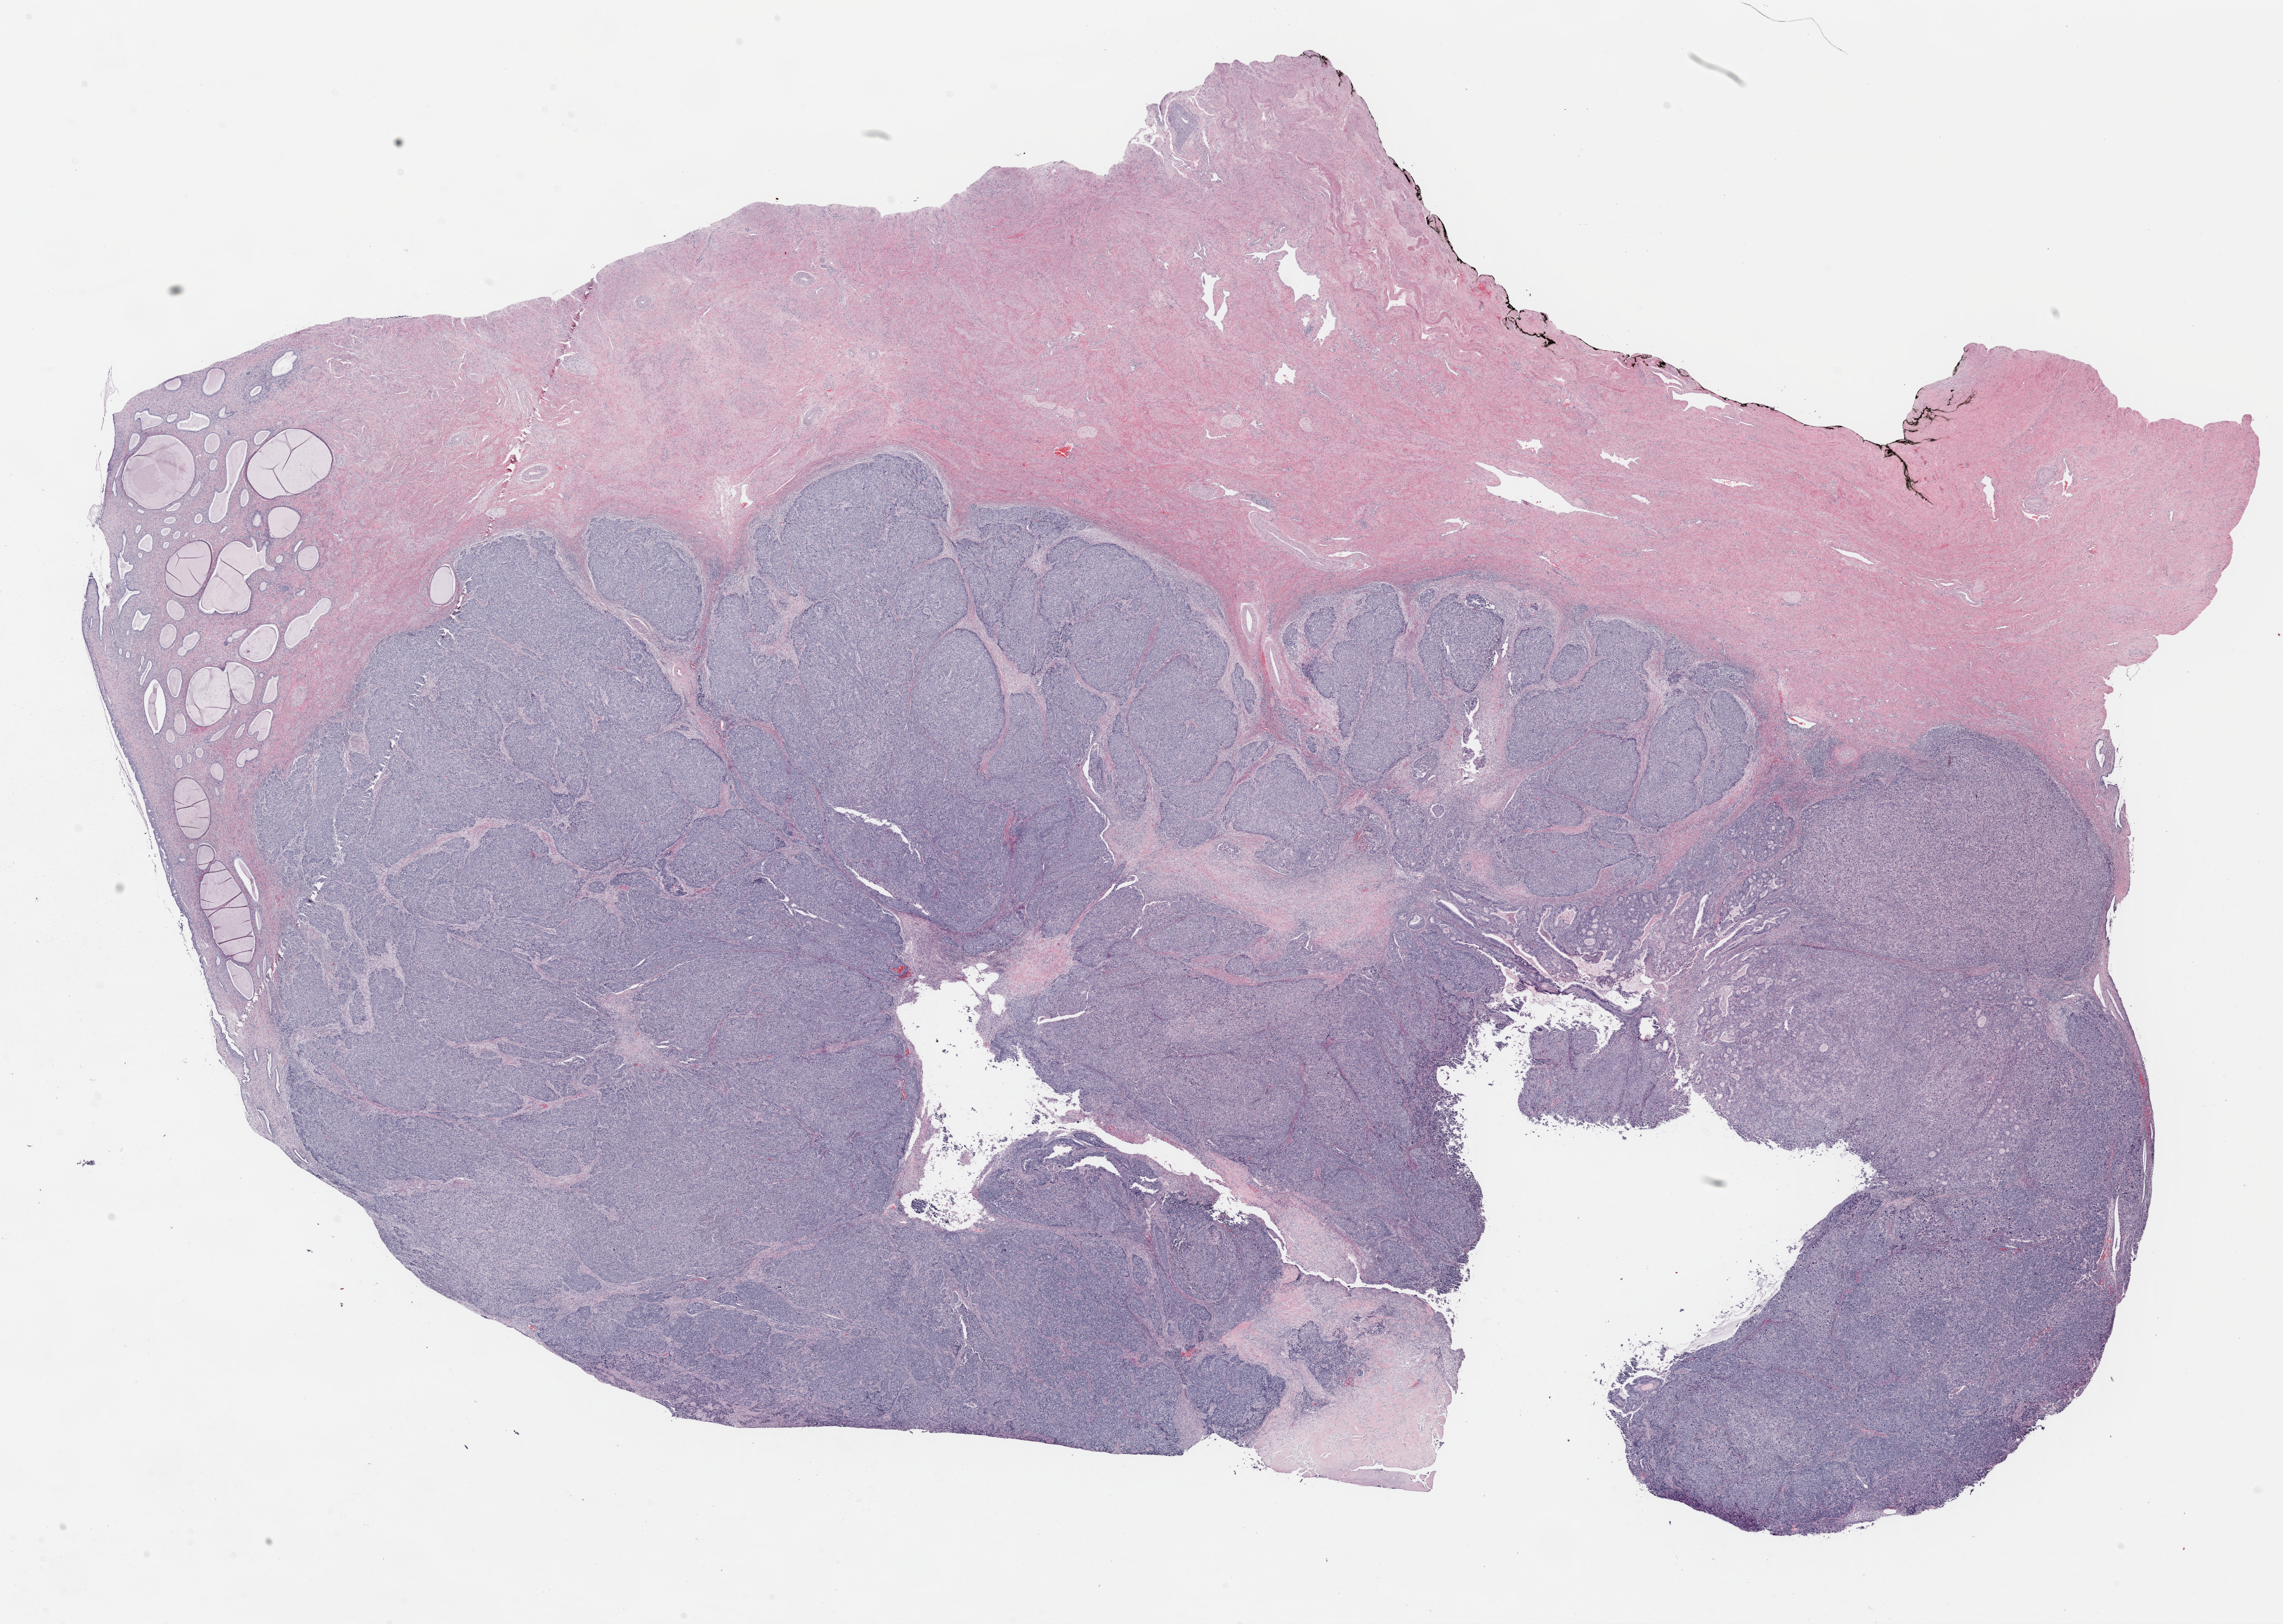
Whole-slide histology image, H&E-stained — shown as a low-resolution overview of the whole scanned area (about 28.3 x 20.1 mm); FFPE section; cervix, primary tumour sample. Female patient; age at initial diagnosis 60 years. Histologic grade: G3 (poorly differentiated).
FIGO stage: IB1. Diagnosis: Adenocarcinoma, endocervical type (cervix uteri). Lymph nodes positive (case pathology): 0 of 18 examined.